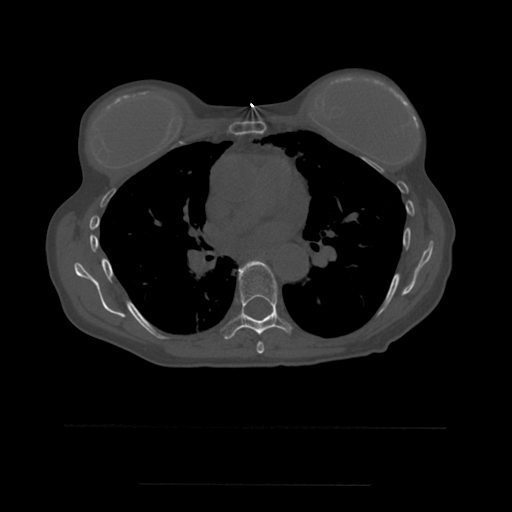
CT including the spine, one axial slice; slice 360 of 544 in the series (ordered by position); bone window (W 1800 / L 400 HU); 1.25 mm slice thickness; 512 × 512 image matrix, field of view 350 × 350 mm. Patient age 58 years. From the clinical record (not read from this slice): primary cancer: lung.
Outlined on this slice (semi-automatically segmented with operator editing):
- T6 vertebra: bounding box [x1, y1, x2, y2] px = [257, 342, 265, 354]
- T7 vertebra: [222, 261, 292, 340]